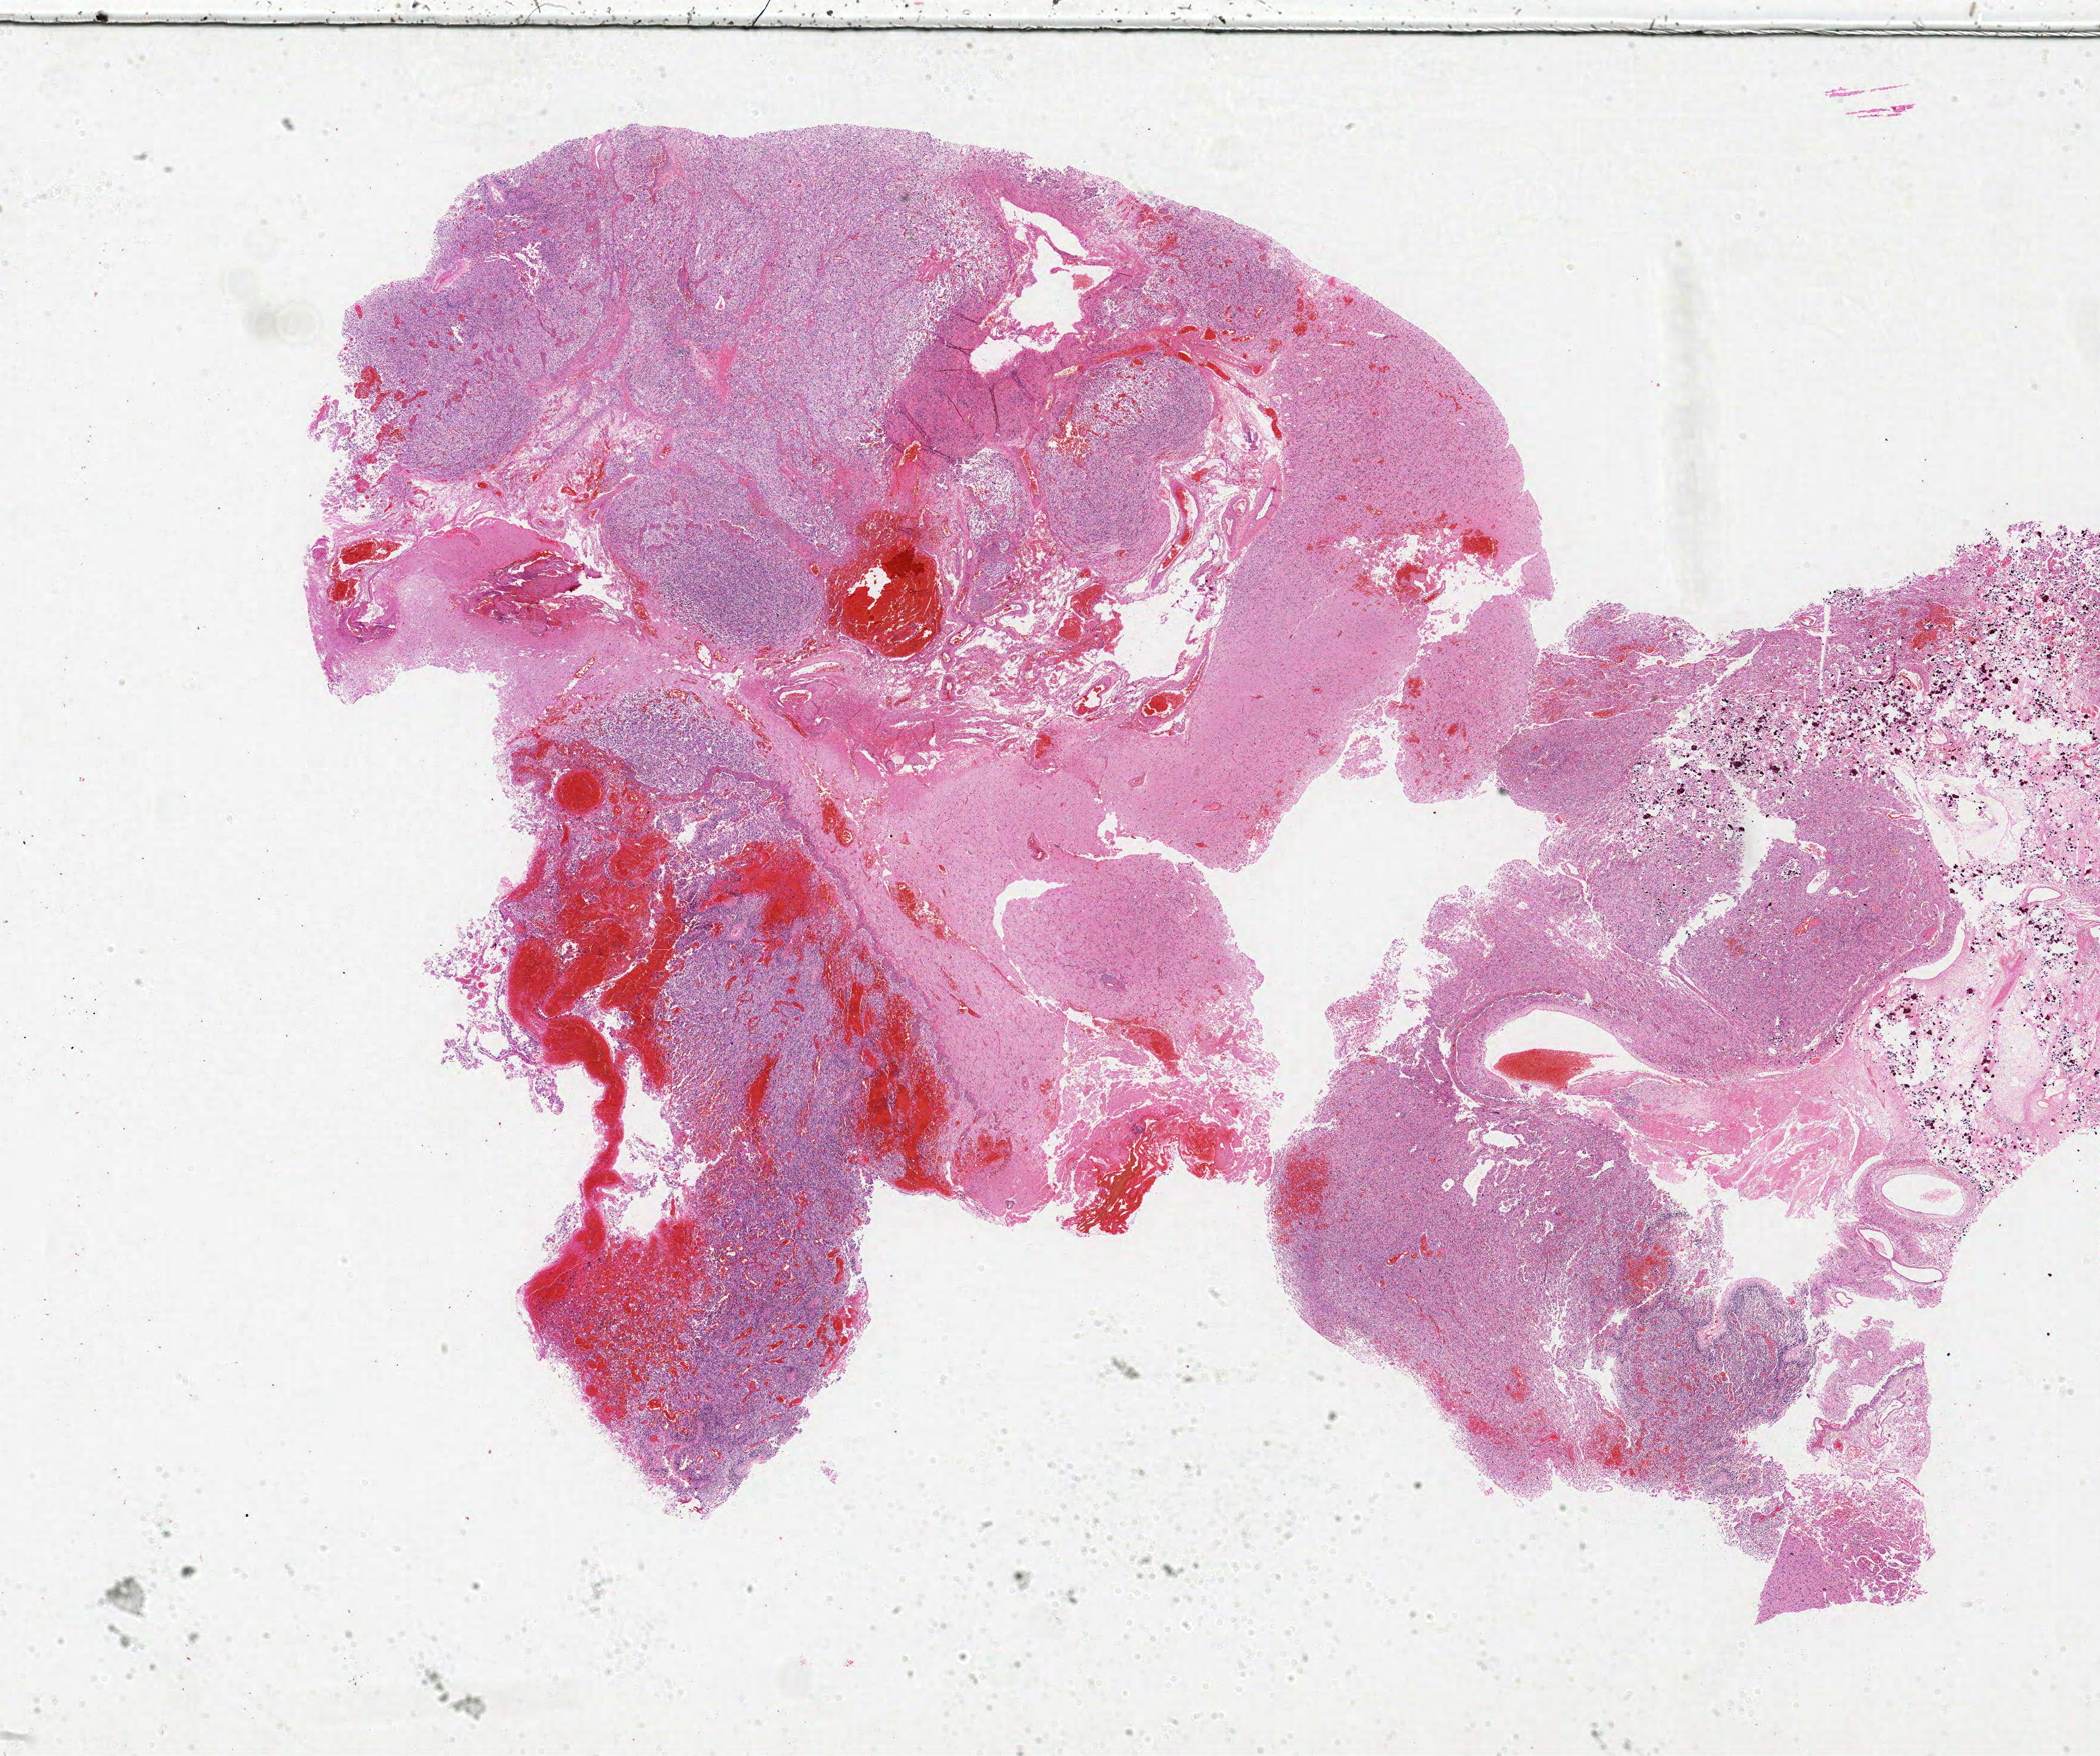
Whole-slide histology image, Hematoxylin and eosin (H&E) stained, low-resolution overview of the scanned area, about 28.0 x 23.4 mm (slide scanned at 20x), FFPE section, sample: primary tumour, brain. Patient: female, age at initial diagnosis 38 years.
Pathologic diagnosis: Glioblastoma.